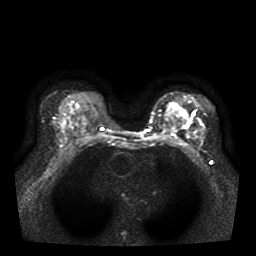
Breast MRI, one axial slice; diffusion-weighted series; image 2 of 4 stored at this slice position (different b-values; order by instance number); 1.5 T; 5 mm slice thickness; 256 × 256 image matrix. Female patient.
Outlined on this slice (manually delineated by an expert):
- tumour on diffusion-weighted imaging: box from (x=187, y=117) to (x=192, y=125) px